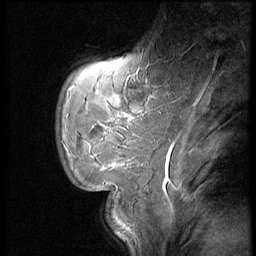
Breast MRI (dynamic contrast-enhanced), one sagittal slice; slice 13 of 62 in the series (ordered by position); dynamic contrast-enhanced series, image 2 of 4 at this slice position (ordered by acquisition); 1.5 T; TE 4.2 ms, TR 9 ms; 2.5 mm slice thickness; 256 × 256 image matrix, field of view 180 × 180 mm. Patient: female, 28 years. From the clinical record (not read from this slice): setting: breast cancer imaged before/during neoadjuvant chemotherapy.
Outlined on this slice (semi-automatic segmentation, software-assisted and operator-edited):
- analysis volume of interest (the breast-tissue region the enhancement analysis was run in; not a lesion): bounding box (x1, y1, x2, y2) in pixels: (59, 54, 150, 183)
- tumour enhancement mask (voxels above the 140 % enhancement threshold inside the analysis volume of interest): (101, 118, 134, 168)